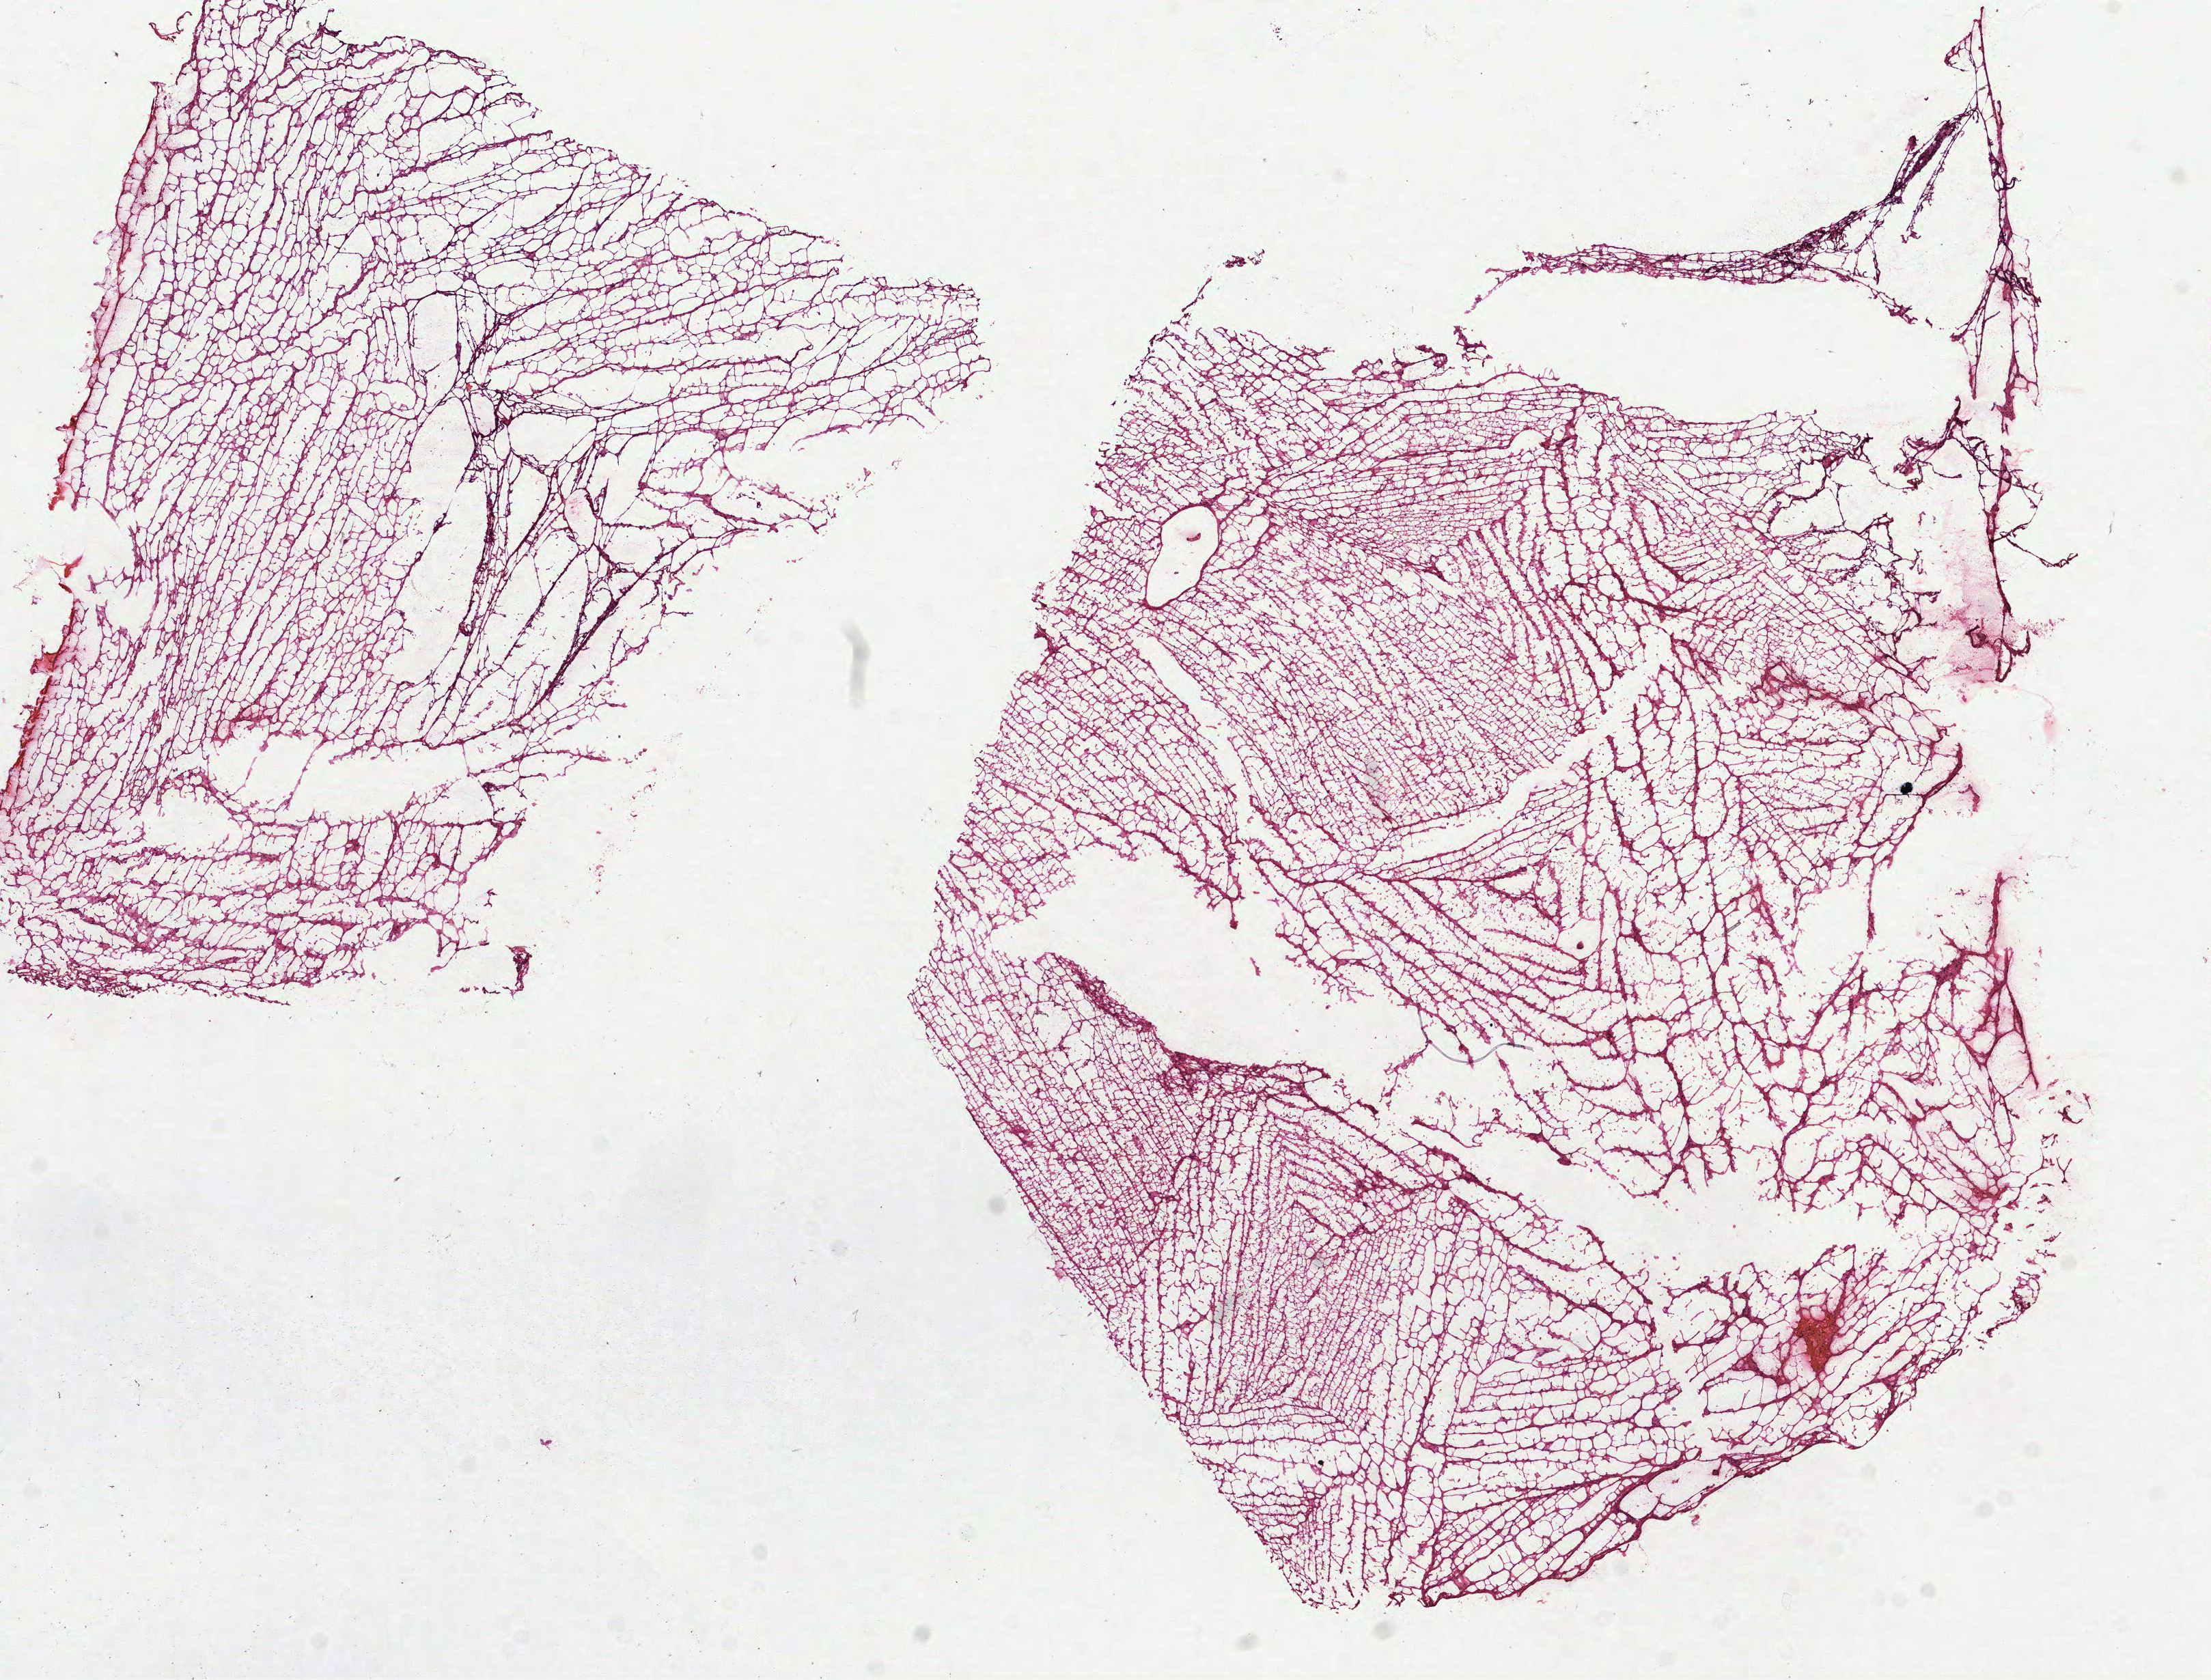
Digitized Hematoxylin and eosin (H&E) stained tissue section (whole slide), shown as a low-resolution overview of the whole scanned area (about 13.1 x 9.9 mm, from a 40x scan). Frozen section. Primary tumour sample from the brain. Female patient; age at initial diagnosis 31 years.
Histologic diagnosis: Astrocytoma, NOS.